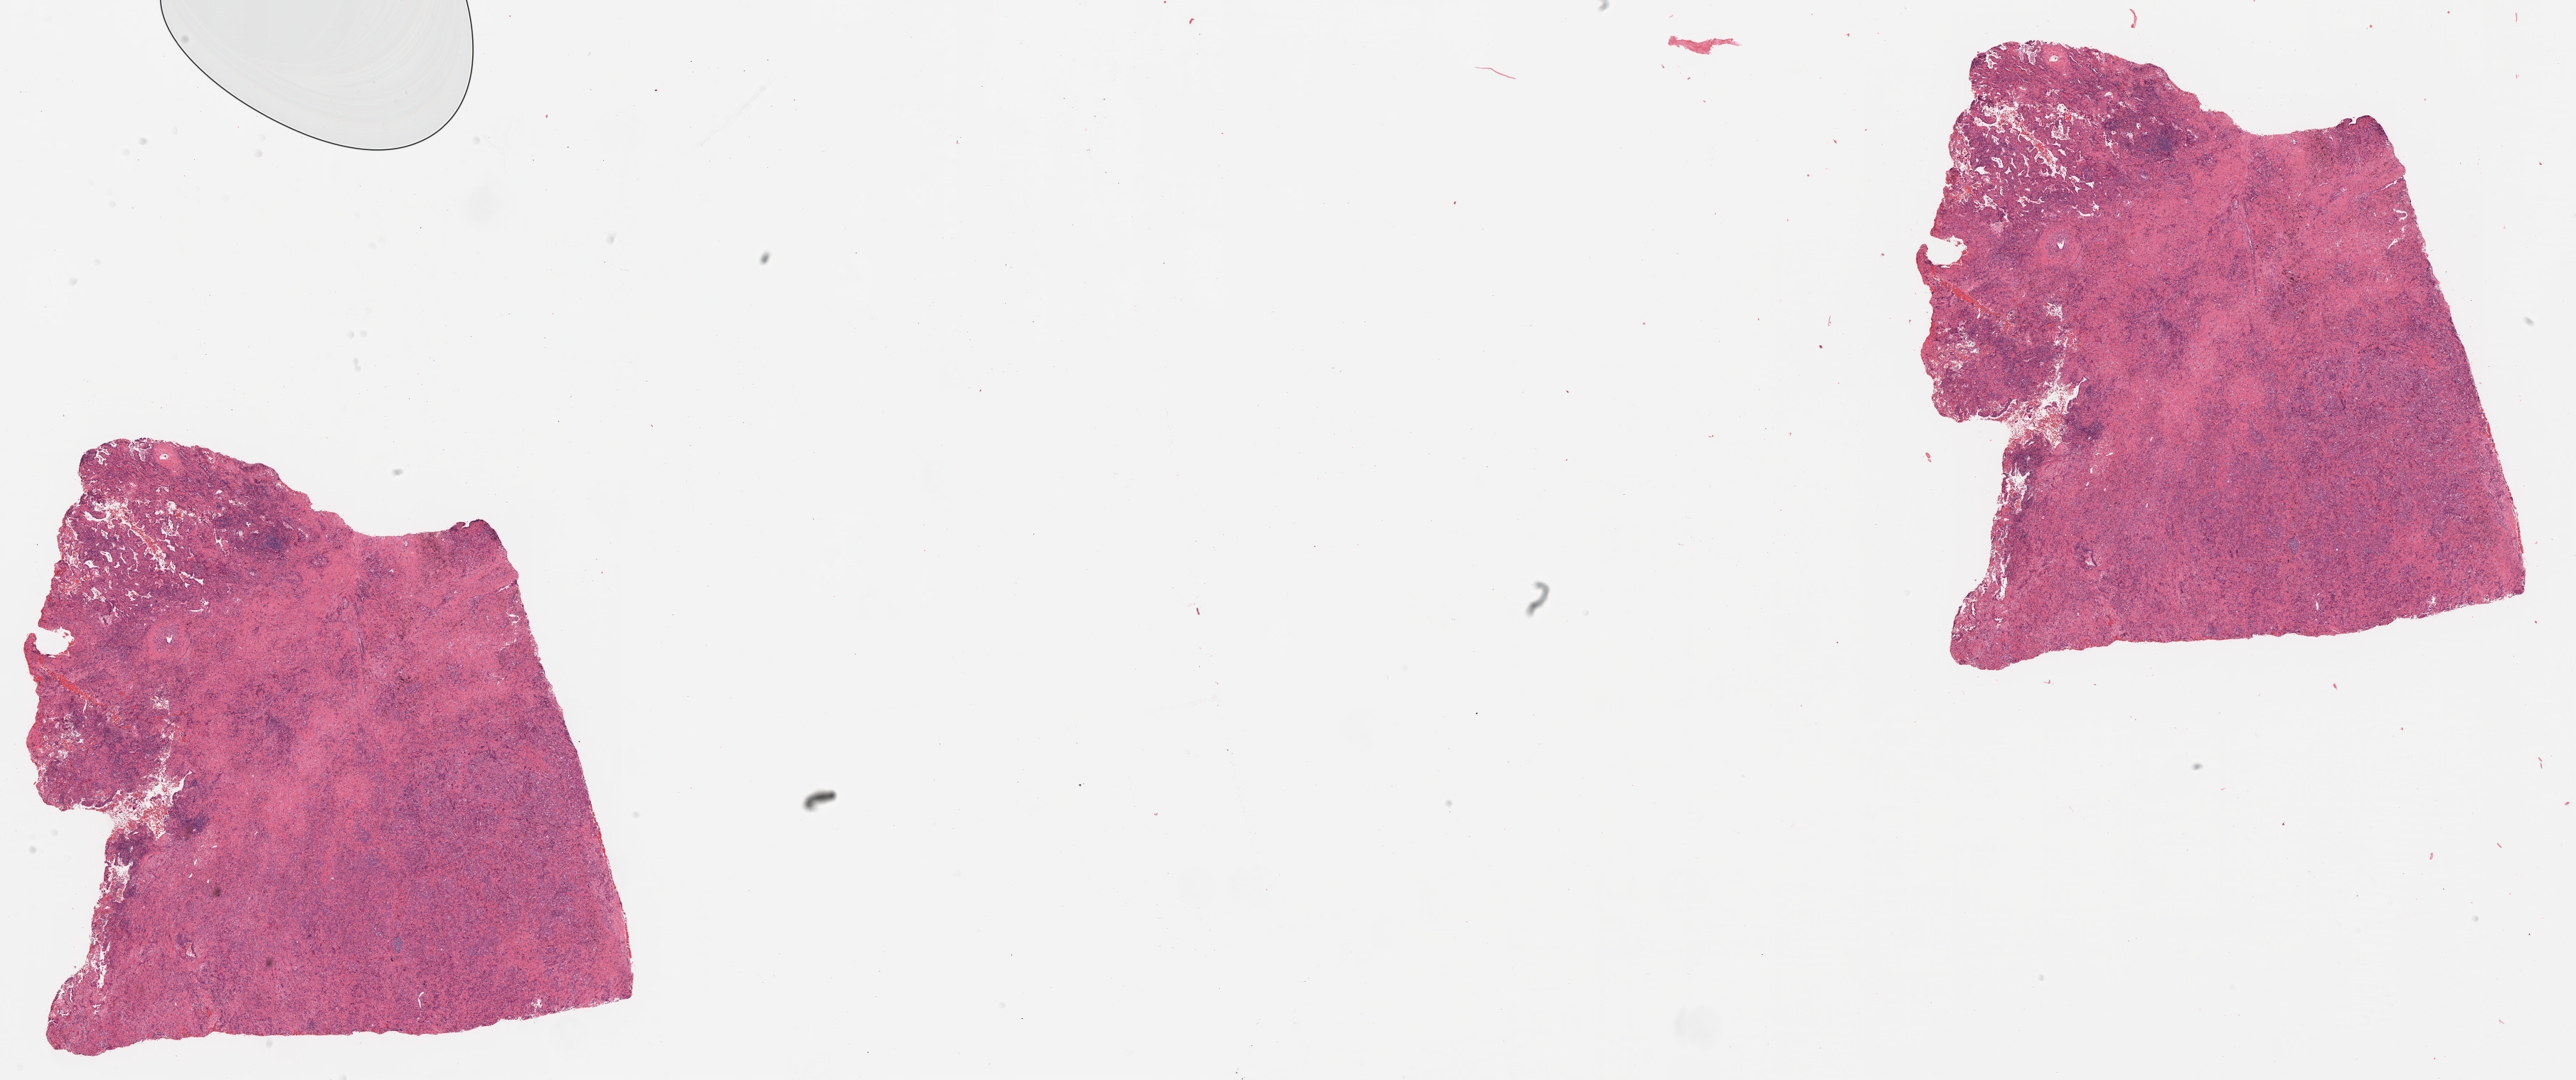
H&E whole-slide image — whole scanned area (about 29.0 x 12.2 mm) shown as a low-resolution overview, FFPE section, lung, primary tumour sample. Female patient.
- laterality: left
- diagnosis: Adenocarcinoma, NOS
- AJCC pathologic stage: IB (7th edition)